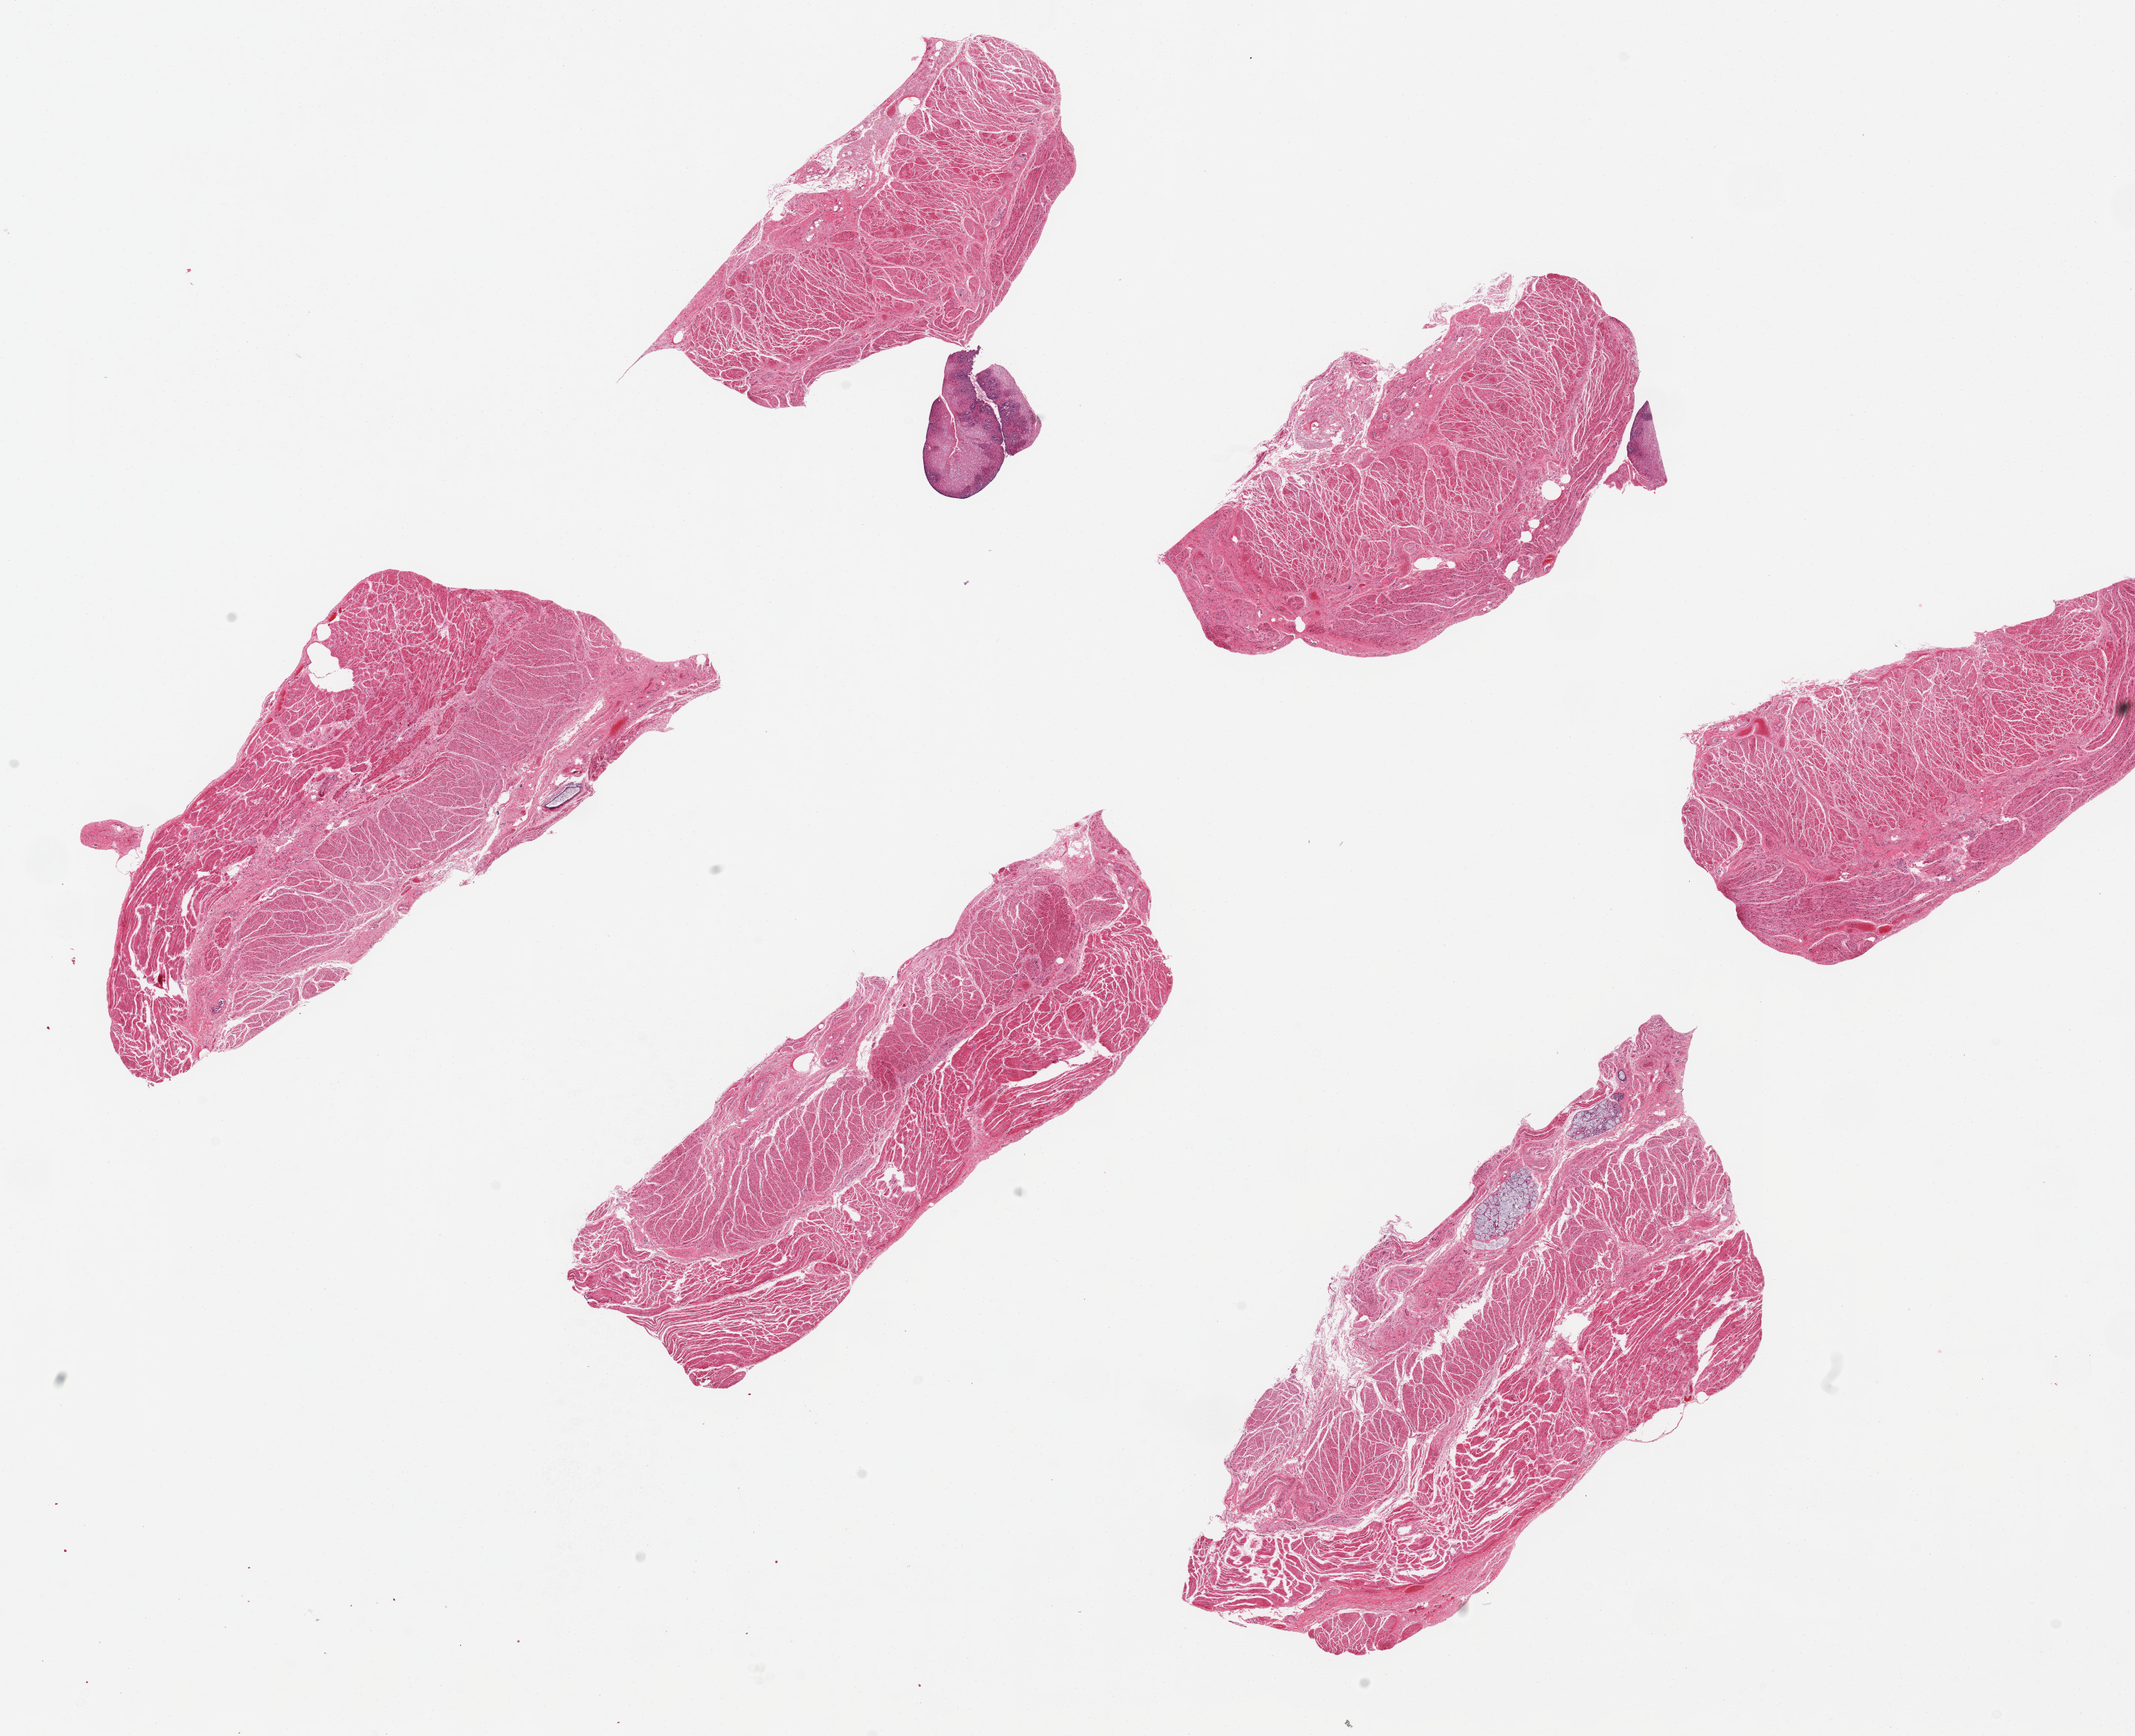
H&E whole-slide image, brightfield — a low-resolution overview of the entire scanned area, about 22.6 x 18.4 mm (slide scanned at 20x), PAXgene-fixed paraffin-embedded (PFPE) section, target tissue: esophageal mucous membrane, tissue donor sample. Donor: female.
Pathologist's review note for this sample: 6 ~6x3mm pieces. Rare minute foci of squamous mucosa.